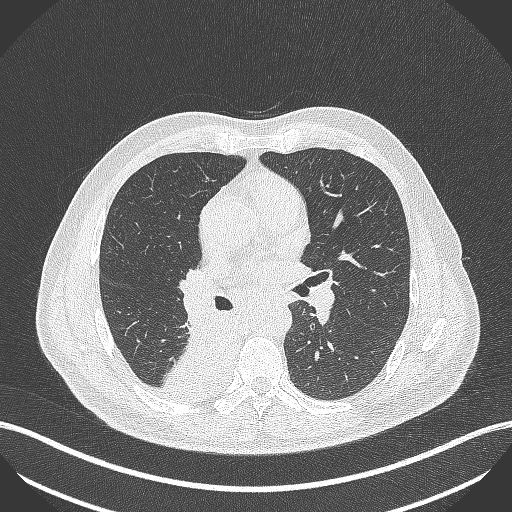
Chest CT, one axial slice; slice 259 of 451 in the series (ordered by position); reconstruction kernel B70f; 100 kVp; lung window (W 1500 / L -600 HU); 1 mm slice thickness; 512 × 512 image matrix, field of view 400 × 400 mm. Male patient, age 61 years. From the clinical record (not read from this slice): clinical TNM (as recorded): T1 N0 M0.
Annotated regions visible in this slice (bounding box drawn by a radiologist):
- lung tumour (recorded histology: small cell carcinoma): bounding box <158,308,241,409> (left, top, right, bottom; pixels)